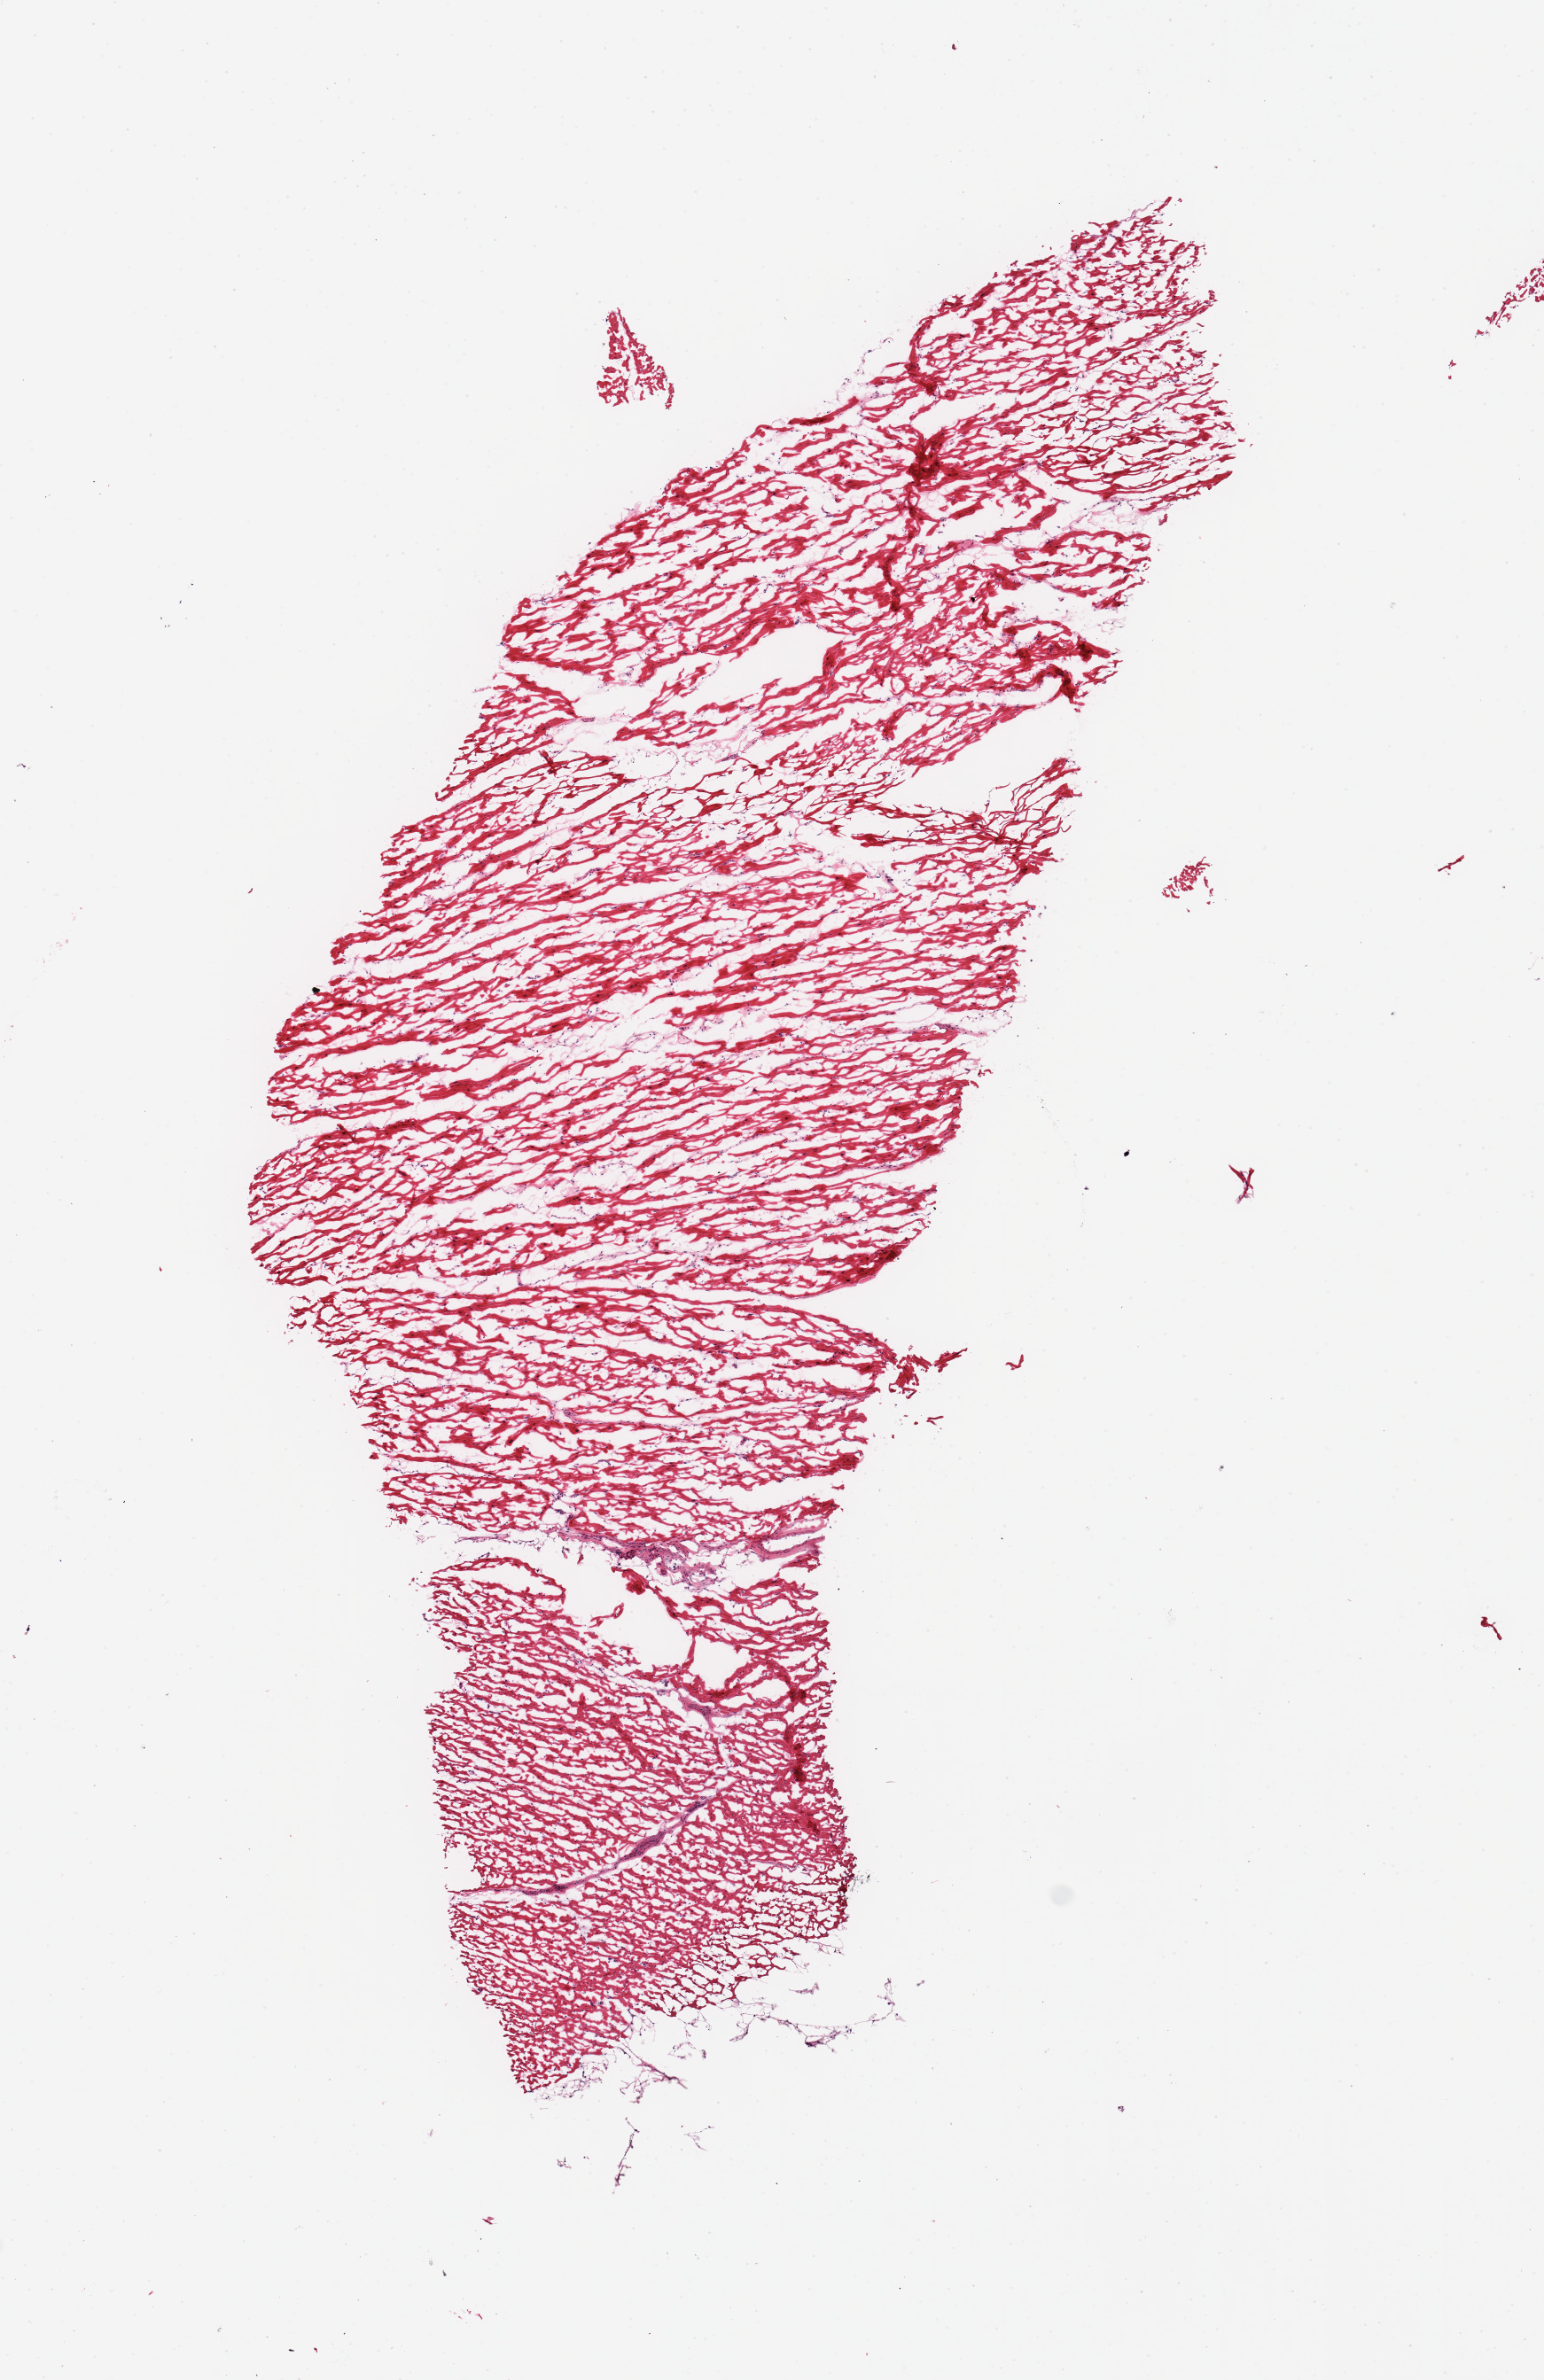
Whole-slide image, haematoxylin and eosin stain, low-resolution overview of the scanned area, about 6.9 x 10.6 mm. Frozen section. Target tissue: heart. Donor tissue sample. Donor sex: female.
• pathologist's review note for this sample: 1 piece; muscle with minimal fat